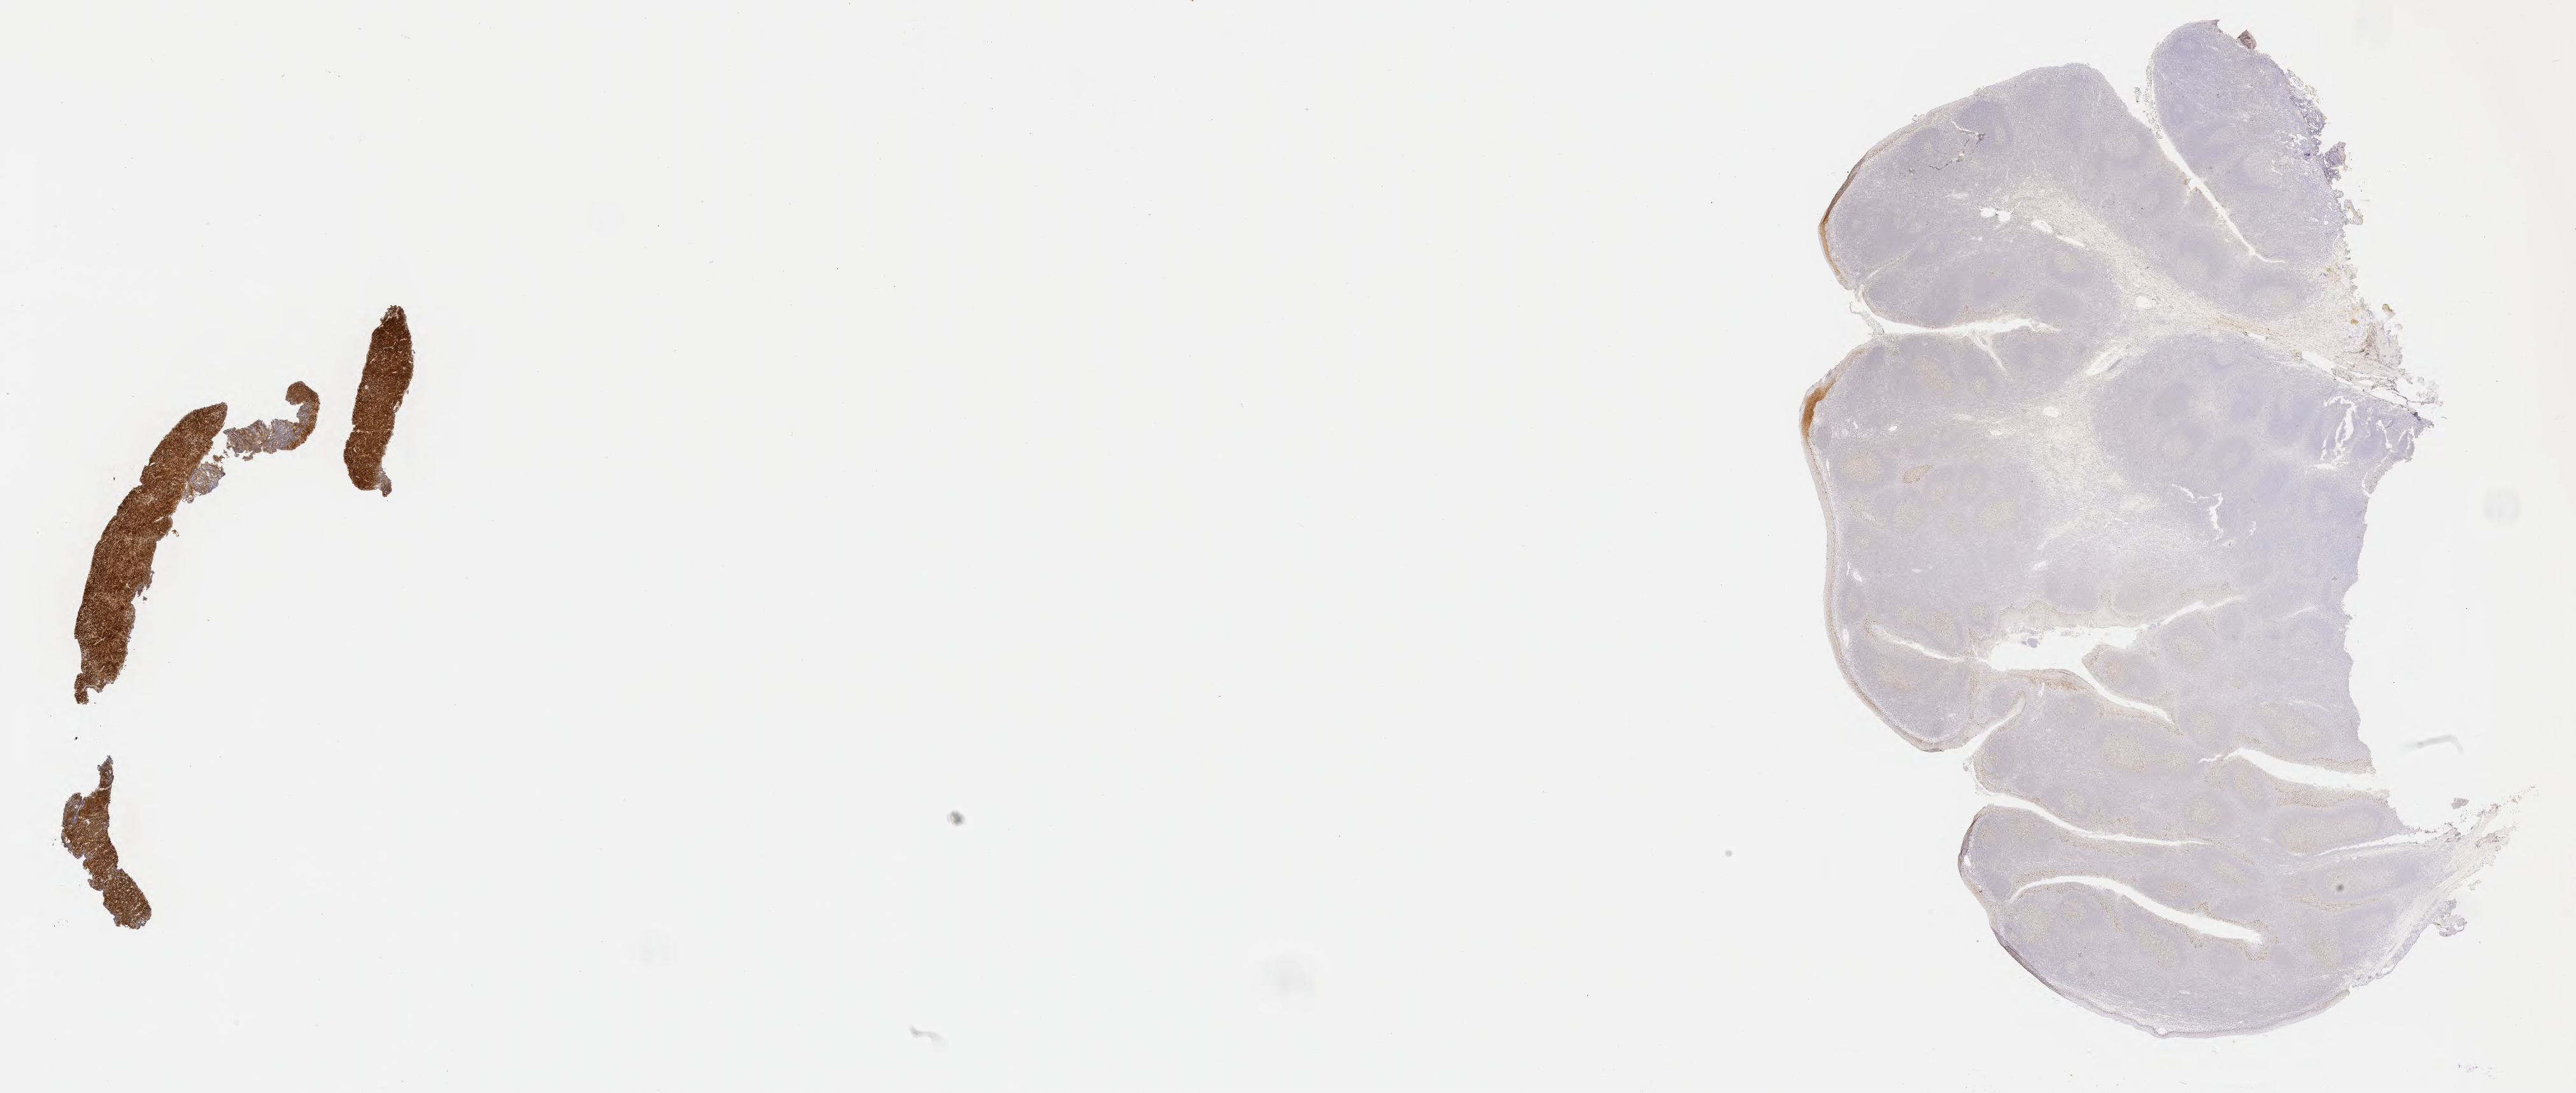
IHC for p53, whole-slide image — whole scanned area (about 32.7 x 13.9 mm) shown as a low-resolution overview. Specimen: tumor tissue. Patient male; age 10 years.
• histologic diagnosis: Diffuse large B-cell lymphoma, NOS